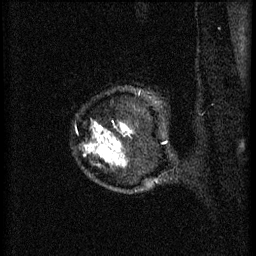
Breast MRI (dynamic contrast-enhanced), one sagittal slice; slice 57 of 60 in the series (ordered by position); 3 images stored at this slice position (order not interpretable as contrast timing); 1.5 T; TE 4.2 ms, TR 11 ms; 256 × 256 image matrix, field of view 180 × 180 mm. Patient: female, 52 years.
Outlined on this slice (semi-automatic segmentation, software-assisted and operator-edited):
- analysis volume of interest (the breast-tissue region the enhancement analysis was run in; not a lesion): bounding box <89,98,167,157> (left, top, right, bottom; pixels)
- tumour enhancement mask (voxels above the 70 % enhancement threshold inside the analysis volume of interest): <91,126,126,153>